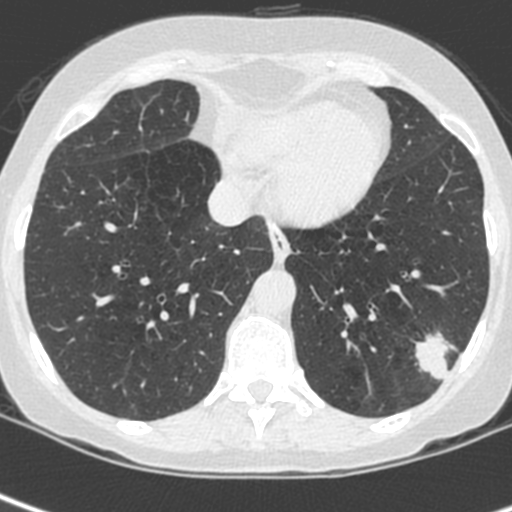
Low-dose screening chest CT, axial slice. Baseline screening round. Lung window (W 1500 / L -600 HU). 1.3 mm slice thickness. 120 kVp. Slice 164 of 252 in the series. Female participant, aged 56 years at enrolment.
Expert-annotated lung lesion, bounding box [x1, y1, x2, y2] px = [409, 327, 472, 389]. Reader record for this screening exam (exam-level; its link to the box is not recorded): non-calcified nodule or mass ≥4 mm, left lower lobe, 37 × 29 mm, spiculated (stellate) margins, ground glass attenuation. Participant outcome: lung cancer diagnosed 91 days after this screen — squamous cell carcinoma, NOS, left lower lobe, poorly differentiated (G3), stage IIIA (AJCC 6th edition), 35 mm at pathology.